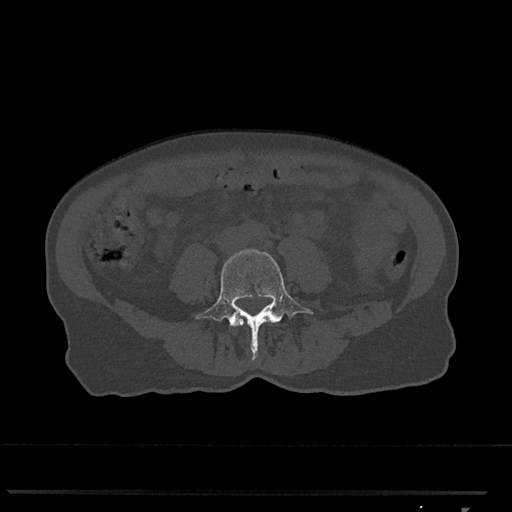
CT including the spine, one axial slice; slice 216 of 793 in the series (ordered by position); reconstruction kernel Br40s/3; bone window (W 1800 / L 400 HU); 0.5 mm slice thickness; 512 × 512 image matrix, field of view 380 × 380 mm. Patient: female, 62 years. Case-level facts recorded for this patient, not image findings: primary cancer: renal.
Structures marked on this image (semi-automatically segmented with operator editing):
- L4 vertebra: bounding box [x1, y1, x2, y2] px = [195, 249, 314, 359]